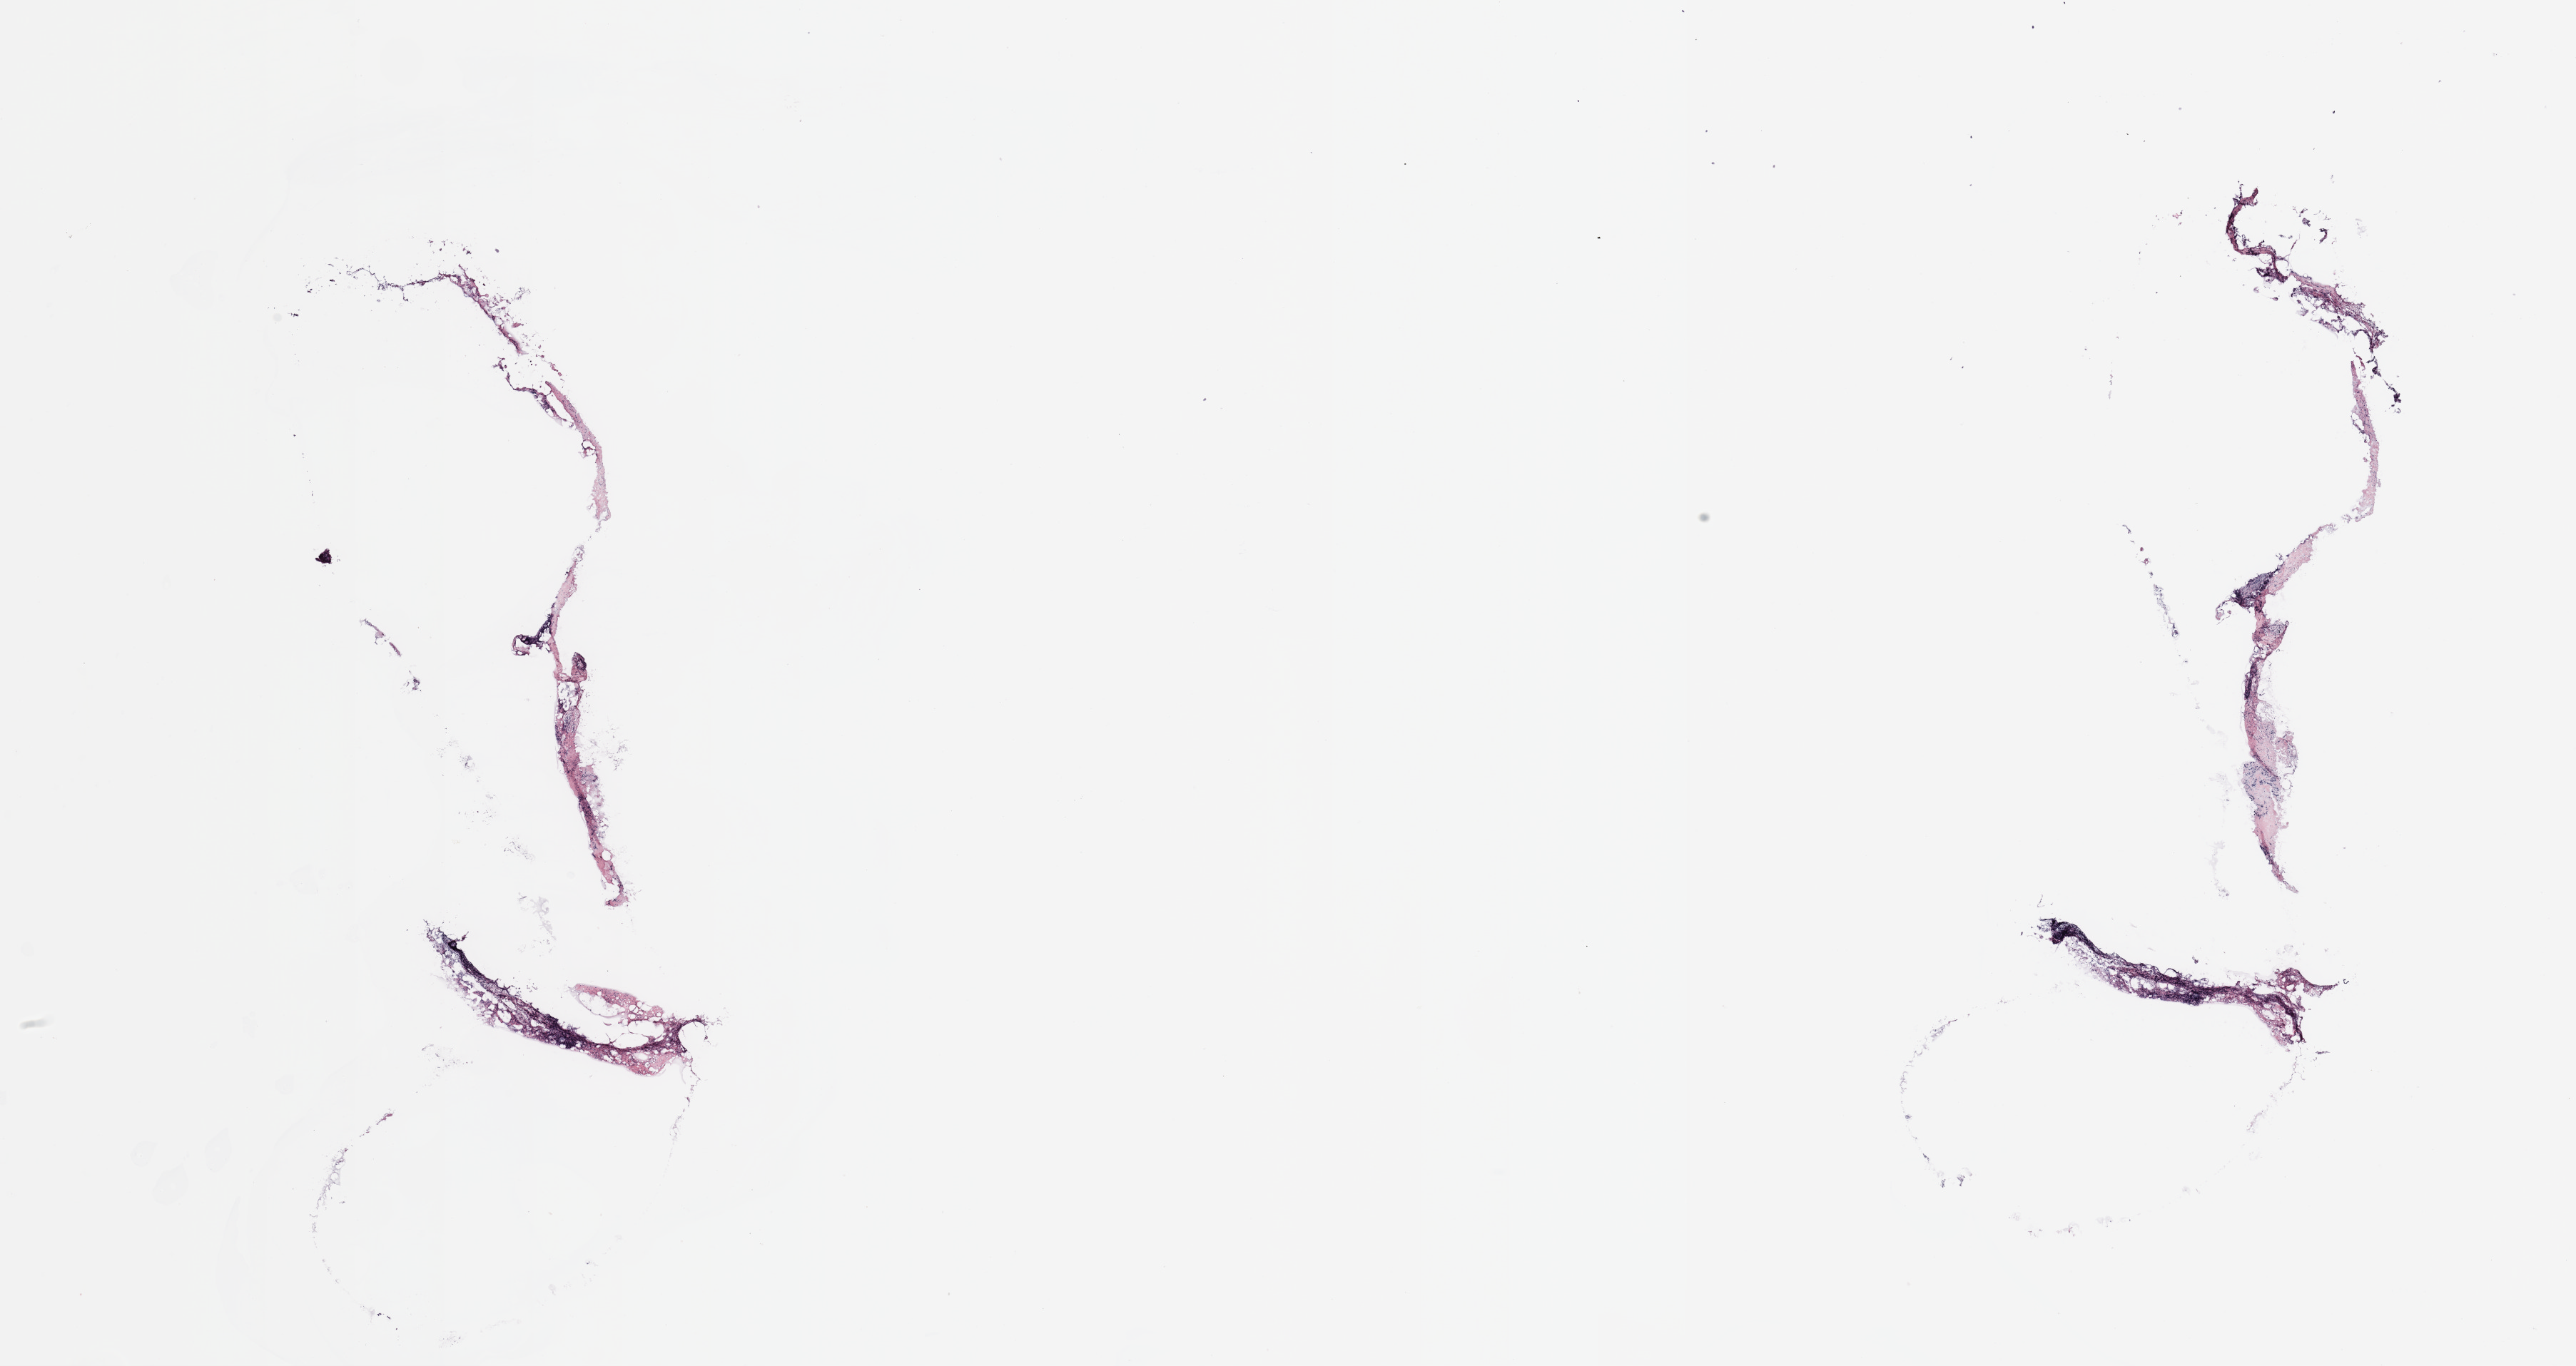
Digitized H&E tissue section (whole slide), low-resolution overview of the scanned area, about 28.5 x 15.1 mm (slide scanned at 20x); breast, tissue type not recorded.
- patient diagnosis (cohort enrolment): breast cancer (breast)